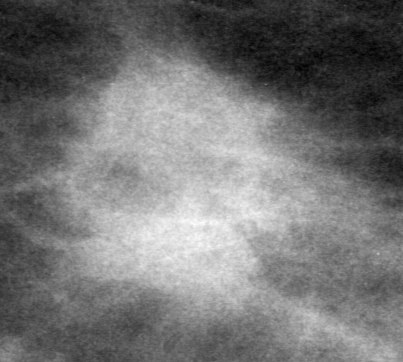
Cropped region of a digitized screen-film mammogram centred on a radiologist-marked abnormality, left breast, CC view.
- Finding: mass, shape irregular, margins ill defined; BI-RADS assessment category 0 (incomplete: needs additional imaging); subtlety rating 4 on a 1 (subtle) to 5 (obvious) scale; pathology (as recorded): malignant.